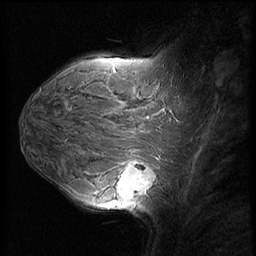
Breast MRI (dynamic contrast-enhanced), one sagittal slice. Position 41 of 60 along the scan axis. Dynamic contrast-enhanced series, image 2 of 3 at this slice position (ordered by acquisition). 1.5 T. TE 4.2 ms, TR 8.9 ms. 2.5 mm slice thickness. 256 × 256 image matrix, field of view 220 × 220 mm. Female patient, age 37 years. From the clinical record (not read from this slice): setting: breast cancer imaged before/during neoadjuvant chemotherapy; receptor status: triple-negative.
Annotated regions visible in this slice (semi-automatic segmentation, software-assisted and operator-edited):
- analysis volume of interest (the breast-tissue region the enhancement analysis was run in; not a lesion): box from (x=114, y=153) to (x=159, y=206) px
- tumour enhancement mask (voxels above the 140 % enhancement threshold inside the analysis volume of interest): (x=120, y=163)–(x=155, y=198)